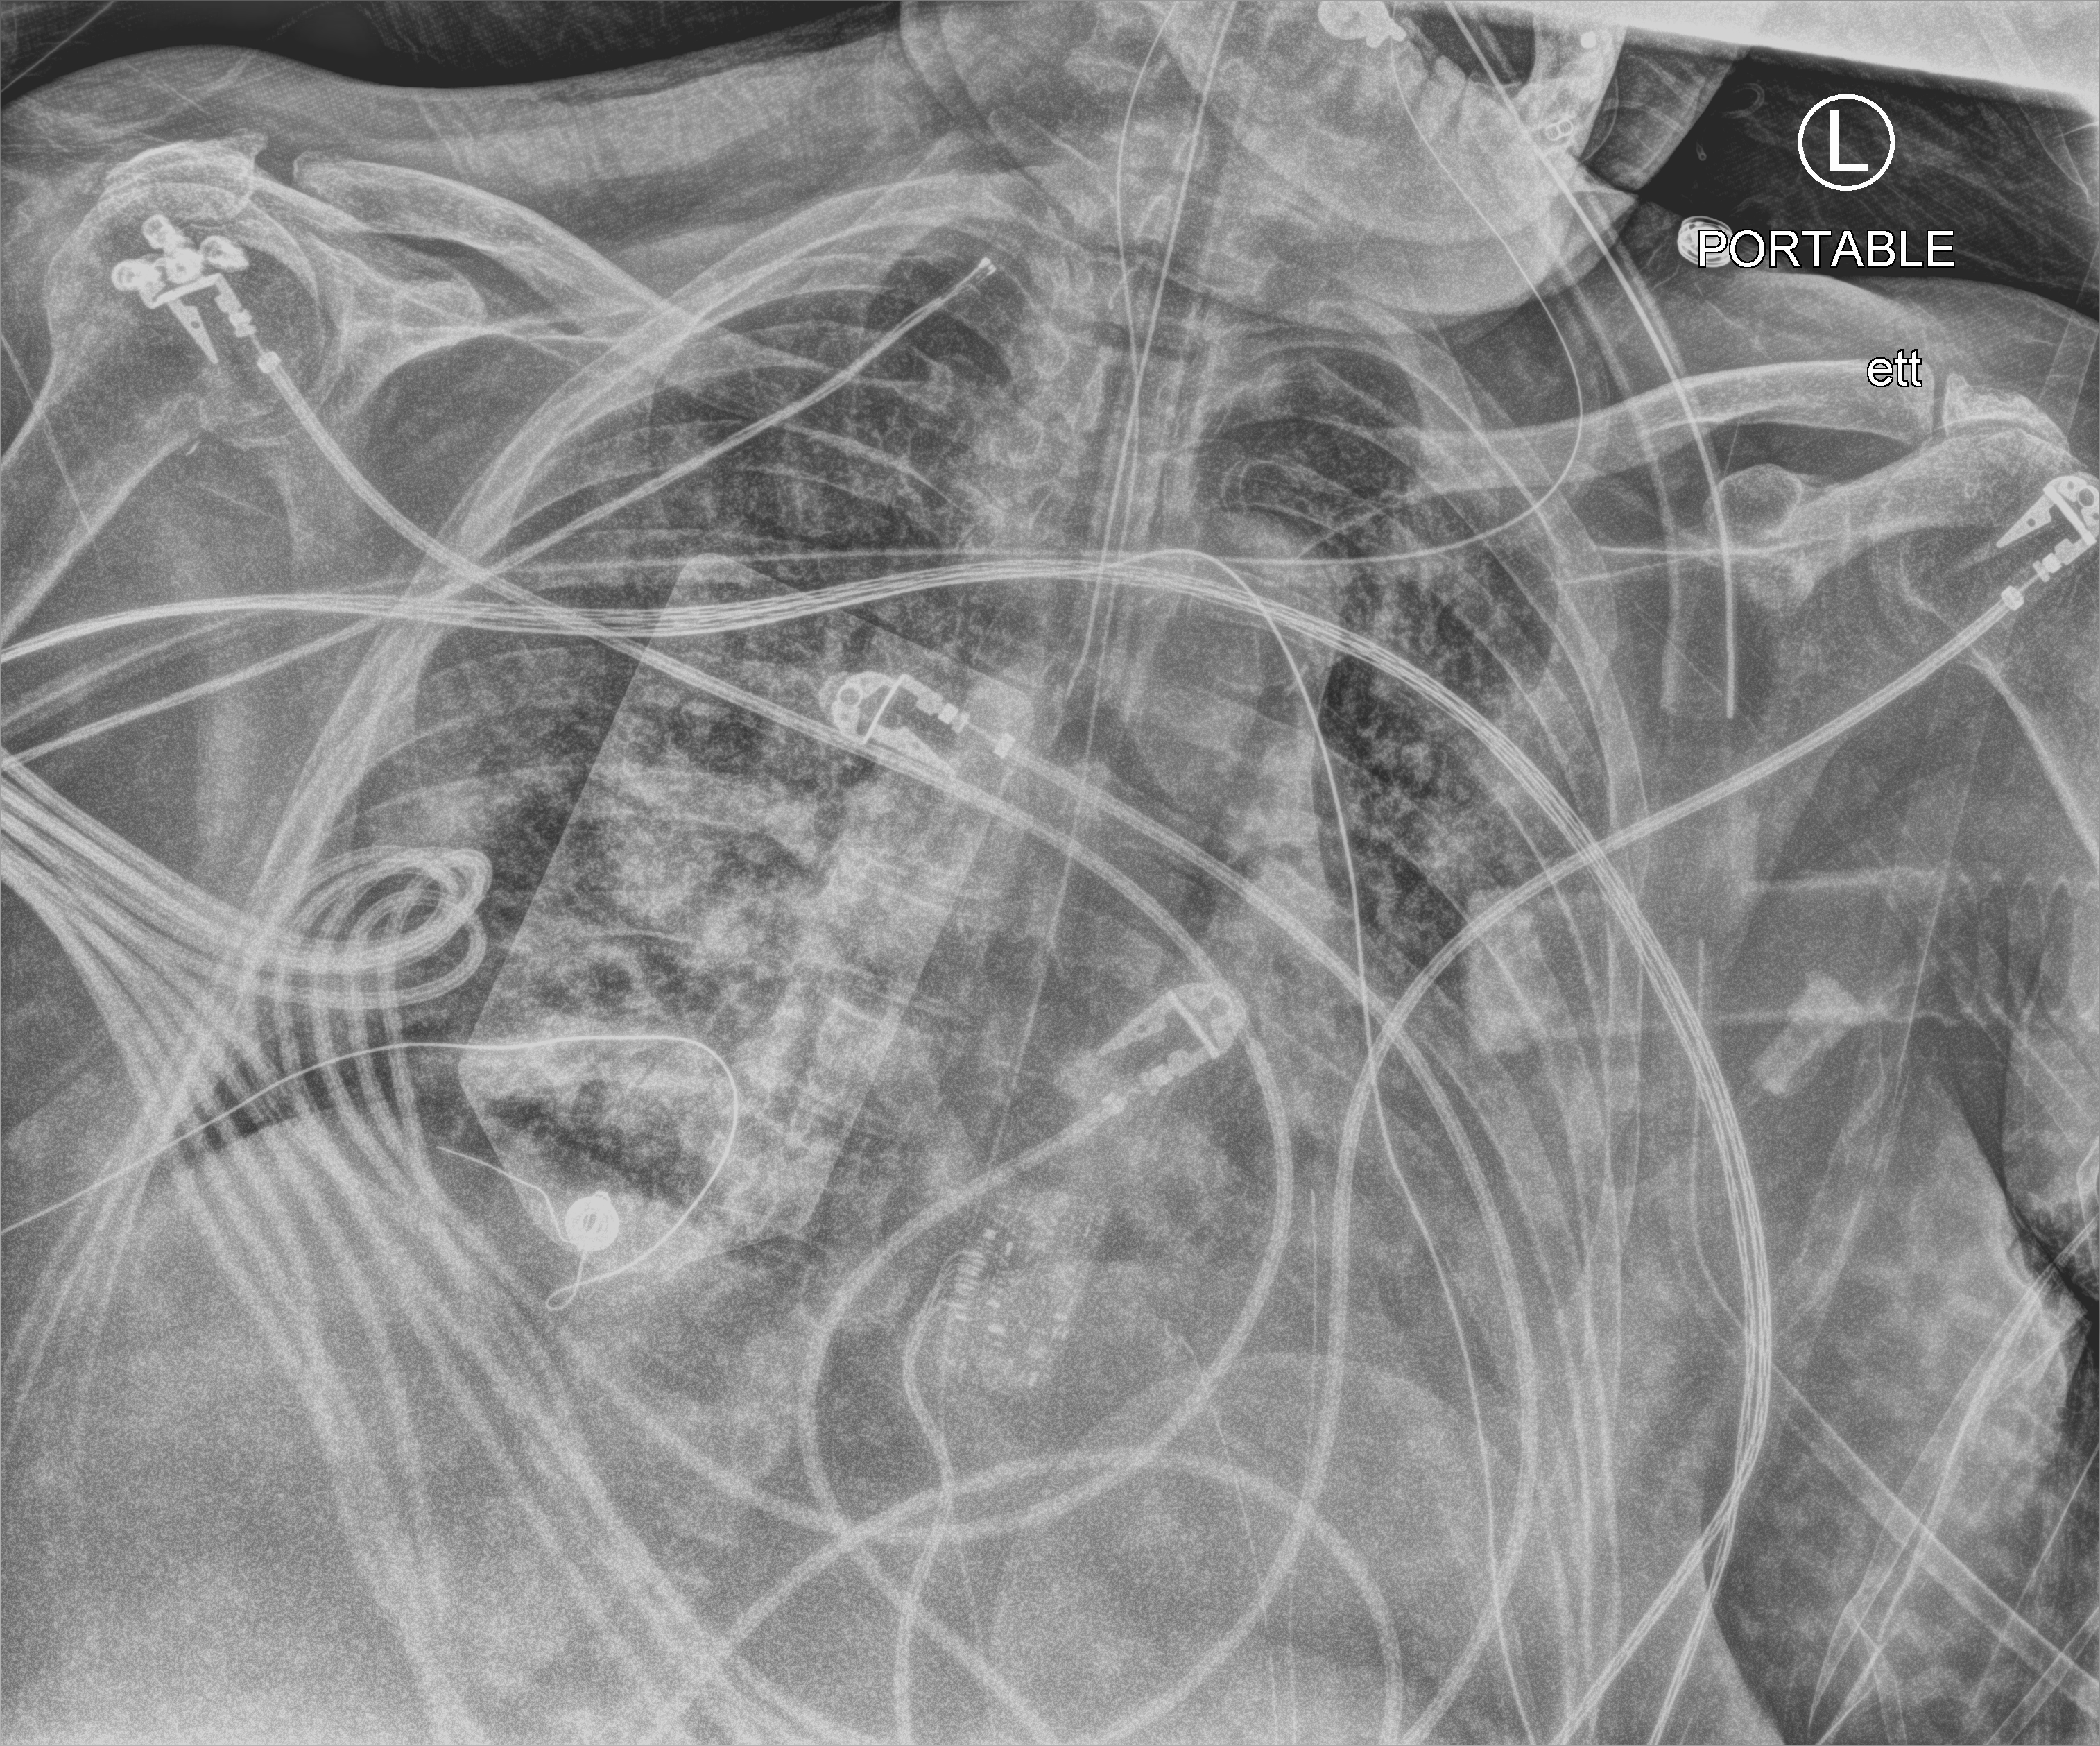
Portable chest radiograph; anteroposterior (AP) projection. Patient hospitalised with COVID-19; female, aged 60–74 years.
Hospital-stay facts (about this admission, not read from this image; timing relative to this image not recorded): COPD (admission record): no.